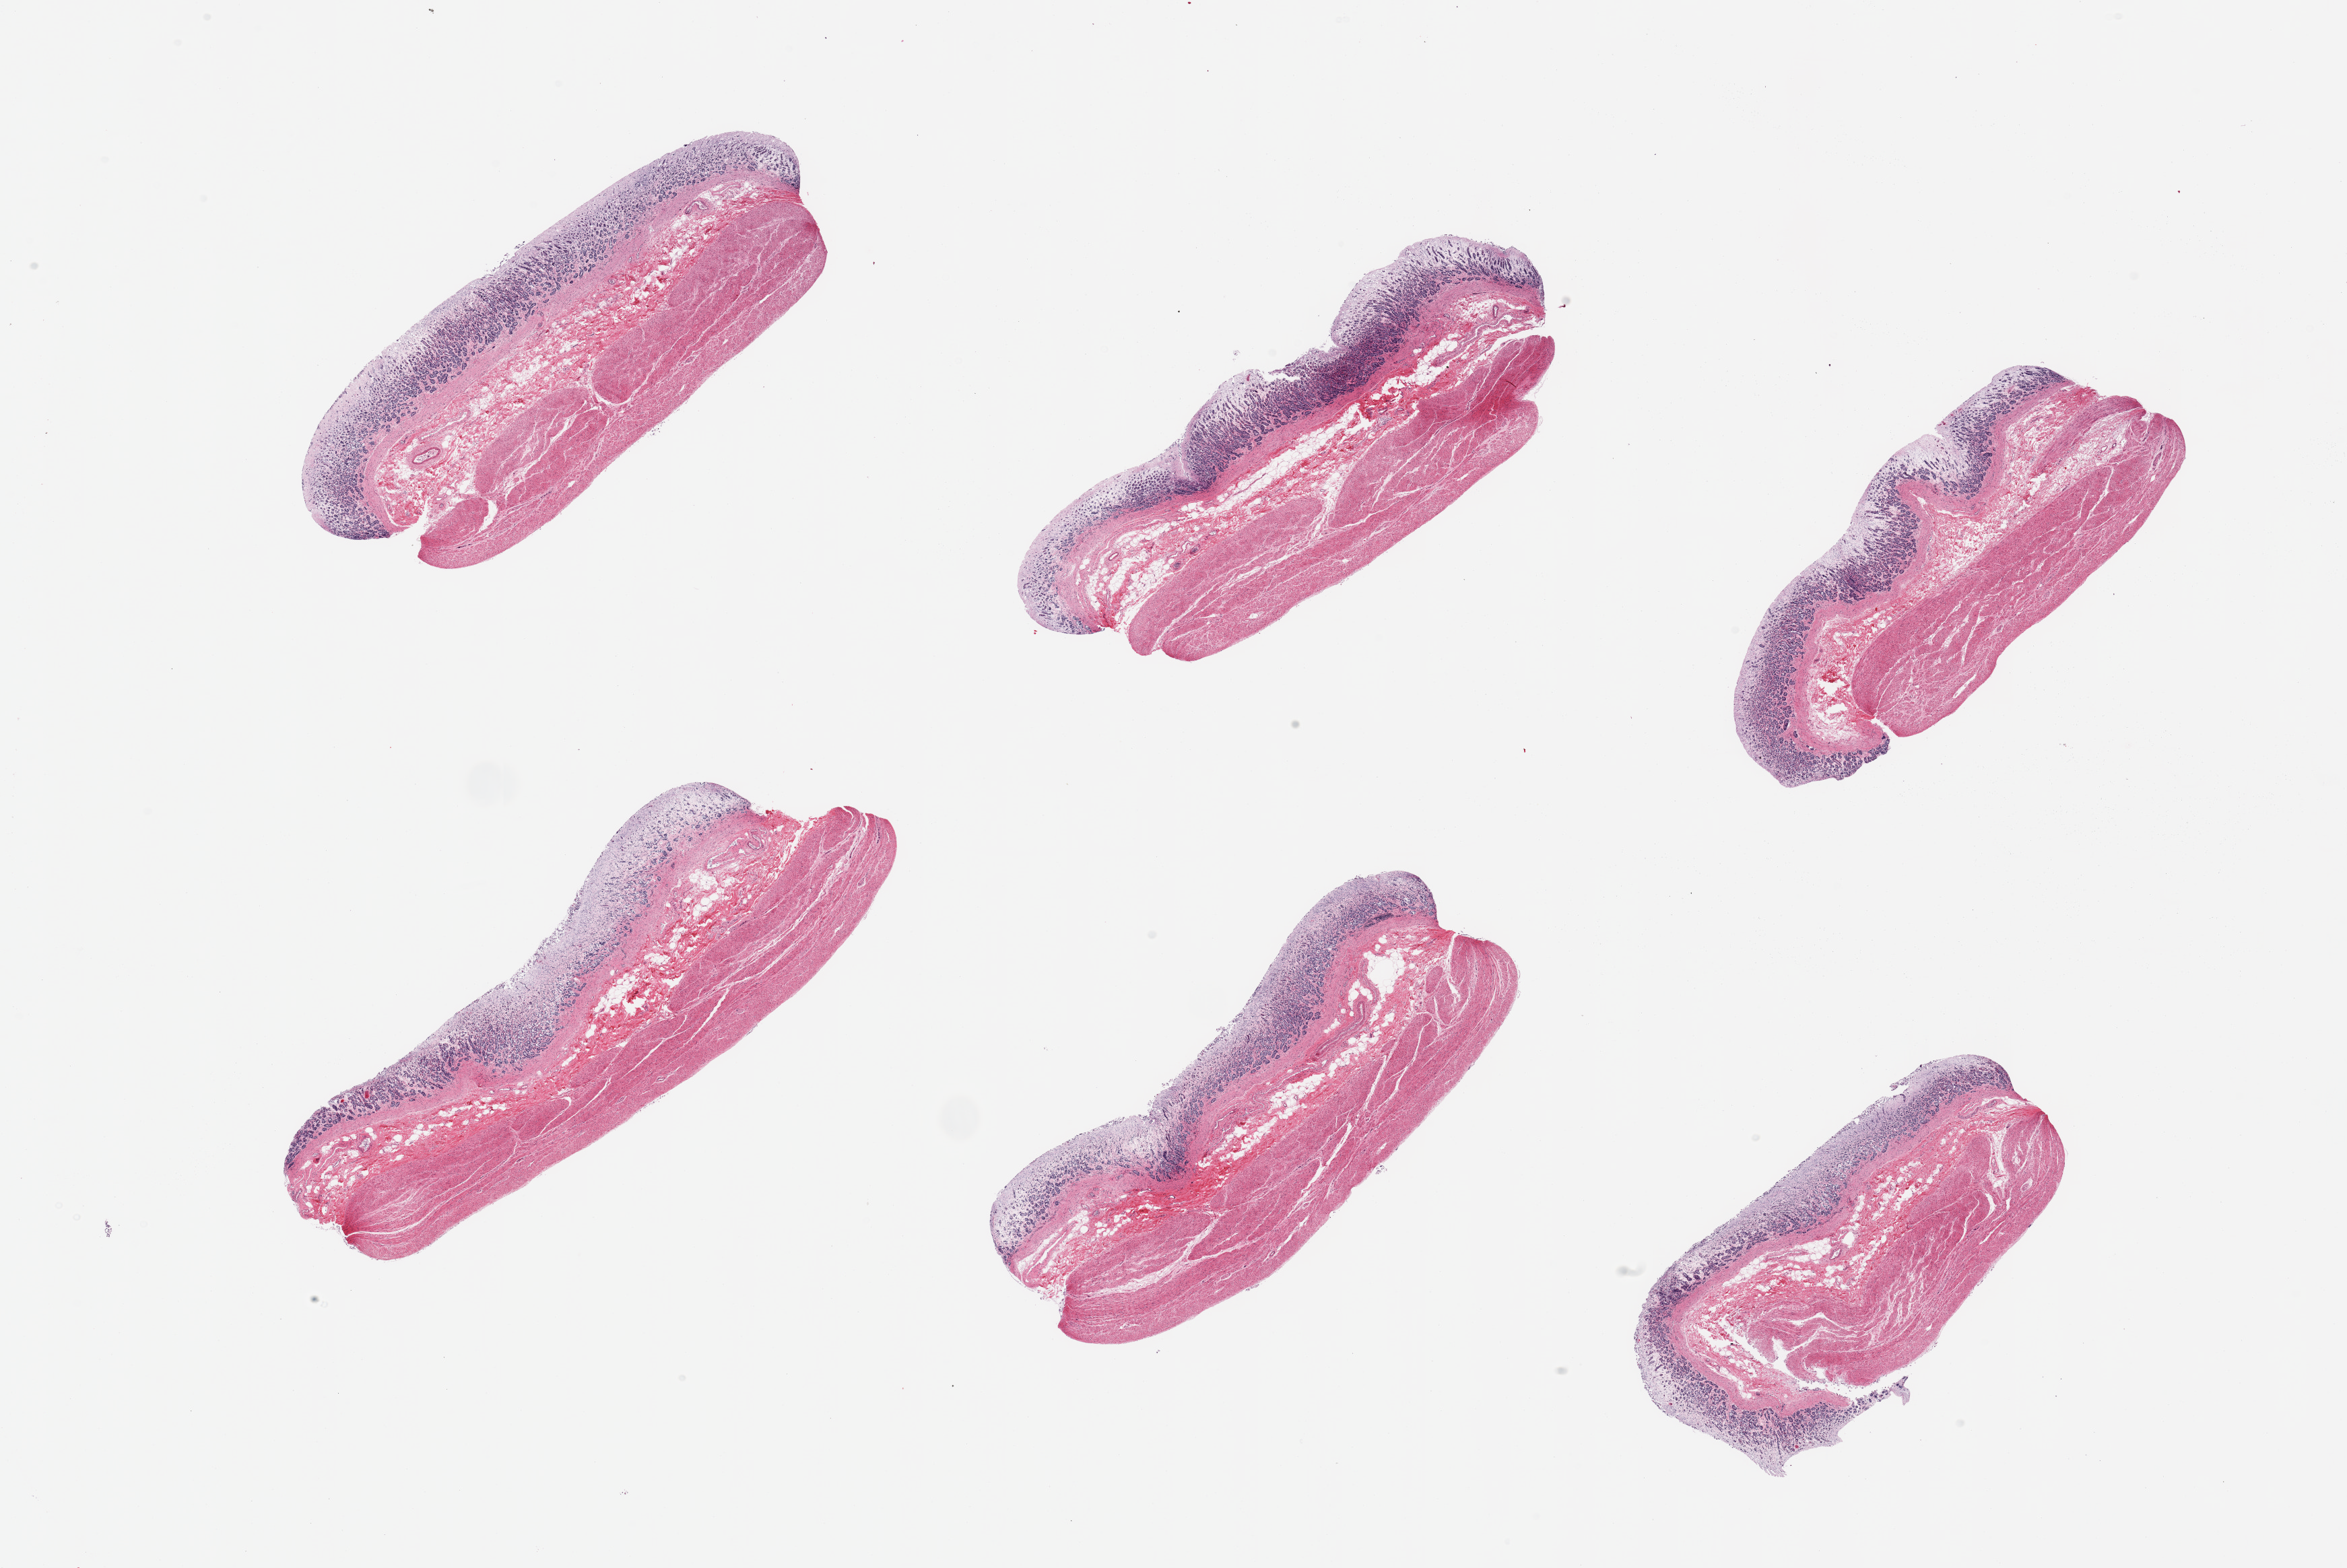
Digitized haematoxylin and eosin-stained section, low-resolution overview of the scanned area, about 27.6 x 18.4 mm (slide scanned at 20x). PAXgene-fixed, paraffin-embedded tissue. Target tissue: stomach. Donor tissue sample. Donor sex: female.
• pathologist's review note for this sample: 6 pieces; mucosa moderately to severely autolyzed; muscularis moderately autolyzed